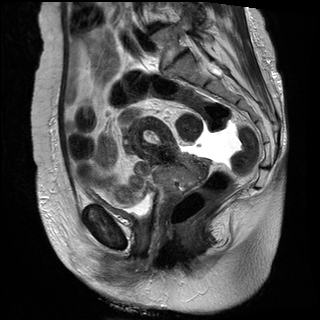
Pelvic MRI for cervical cancer, one sagittal slice. Position 16 of 30 along the scan axis. T2-weighted. 1.5 T. TE 89 ms, TR 2930 ms. 4 mm slice thickness. 320 × 320 image matrix, field of view 260 × 260 mm. Female patient, age 61 years.
Structures marked on this image (outlined manually by an expert reader):
- uterus and cervix: bounding box <129,116,212,204> (left, top, right, bottom; pixels)